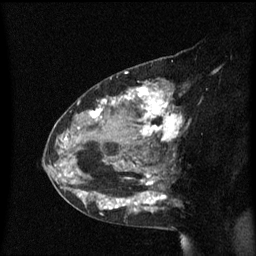
Breast MRI (dynamic contrast-enhanced), one sagittal slice; slice 37 of 60 in the series (ordered by position); dynamic contrast-enhanced series, image 2 of 3 at this slice position (ordered by acquisition); 1.5 T; TE 4.2 ms, TR 8.4 ms; 2 mm slice thickness; 256 × 256 image matrix. Female patient, age 48 years. From the clinical record (not read from this slice): setting: breast cancer imaged before/during neoadjuvant chemotherapy; receptor status: HR-positive, HER2-negative.
Outlined on this slice (semi-automatically segmented with operator editing):
- analysis volume of interest (the breast-tissue region the enhancement analysis was run in; not a lesion): bounding box [x1, y1, x2, y2] px = [80, 78, 189, 221]
- tumour enhancement mask (voxels above the 70 % enhancement threshold inside the analysis volume of interest): [80, 83, 183, 212]